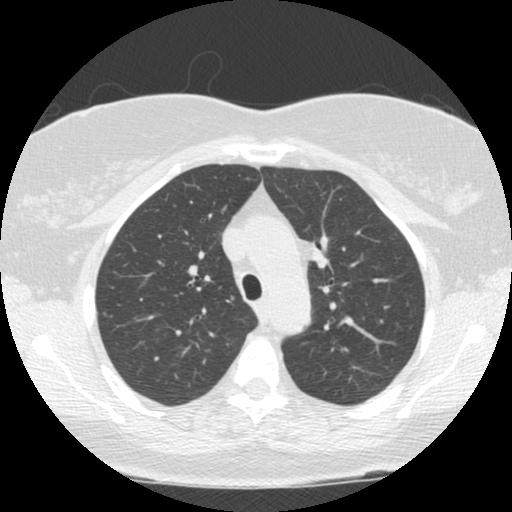
Axial slice from a low-dose chest CT screening exam, second annual screen, lung window (W 1500 / L -600 HU), standard (soft-tissue) reconstruction kernel (STANDARD), 512 × 512 image matrix. Female participant, aged 66 years at enrolment.
- Lesion marked by an expert reader, box from (x=289, y=232) to (x=345, y=280) px.
- Reader record for this screening exam (exam-level; its link to the box is not recorded): non-calcified nodule or mass ≥4 mm, left upper lobe, 12 × 9 mm, smooth margins, soft tissue attenuation, pre-existing on the prior screen: no.
- Official screen result: positive, other.
- Participant outcome: lung cancer diagnosed 196 days after this screen — small cell carcinoma, NOS, left upper lobe, stage IIIA (AJCC 6th edition), 50 mm at pathology.